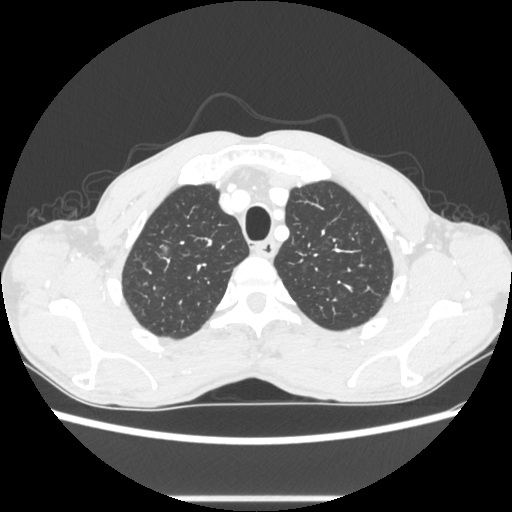
Chest CT, one axial slice; position 238 of 289 along the scan axis; 100 kVp; lung window (W 1500 / L -600 HU); 1.25 mm slice thickness; 512 × 512 image matrix, field of view 350 × 350 mm. Patient: male, 54 years. Case-level facts recorded for this patient, not image findings: clinical TNM (as recorded): T1a N0 M0.
Structures marked on this image (bounding box drawn by a radiologist):
- lung tumour (recorded histology: adenocarcinoma): bounding box [x1, y1, x2, y2] px = [153, 242, 174, 268]